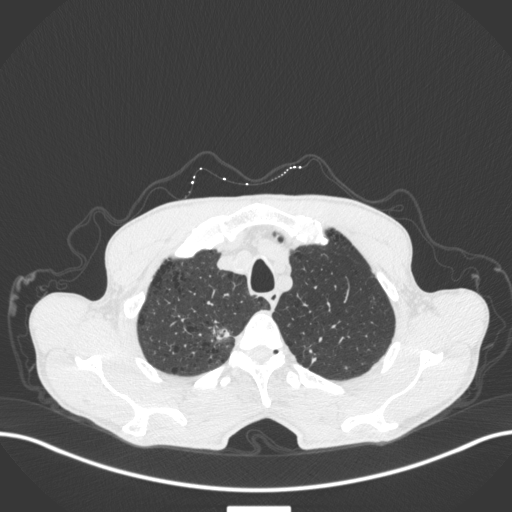
Chest CT, one axial slice; slice 367 of 445 in the series (ordered by position); reconstruction kernel B31f; lung window (W 1500 / L -600 HU); 1 mm slice thickness; 512 × 512 image matrix. Patient: male, 70 years. Case-level facts recorded for this patient, not image findings: clinical TNM (as recorded): T1a N0 M0; histopathological grade: G1-2.
Annotated regions visible in this slice (rectangle marked by the reading radiologist):
- lung tumour (recorded histology: adenocarcinoma): box from (x=201, y=314) to (x=235, y=346) px